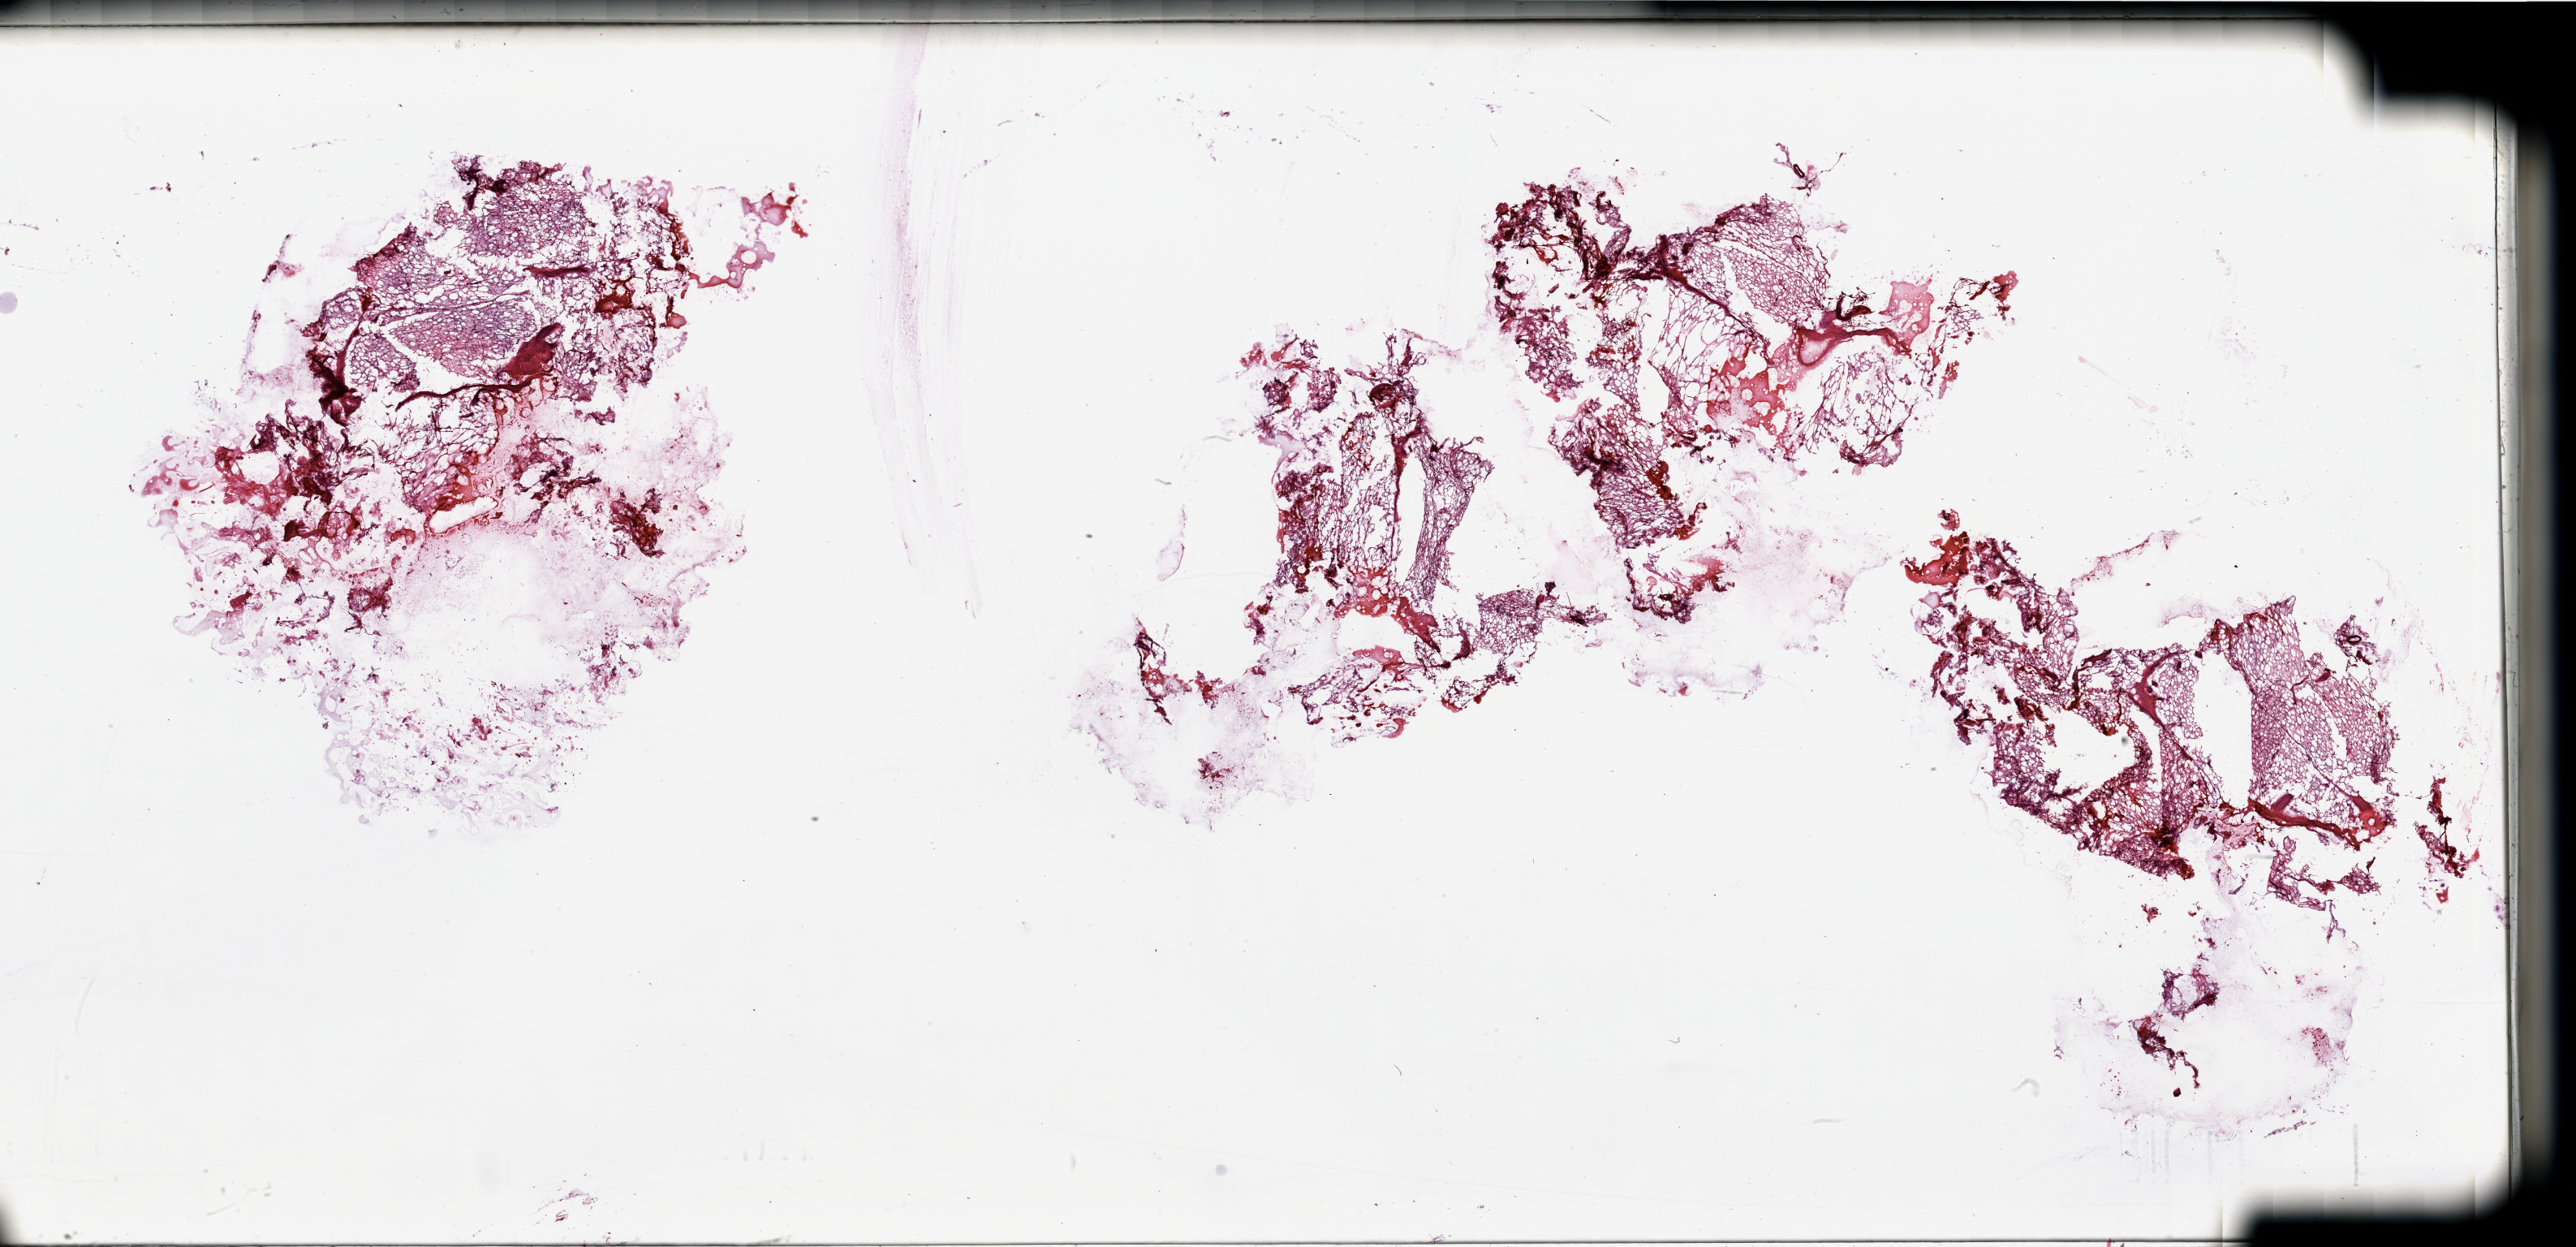
Whole-slide histology image, H&E — low-resolution overview of the scanned area, about 50.2 x 24.3 mm (slide scanned at 20x); tumour tissue sample, kidney. 74-year-old female patient. Histologic grade: G2 (moderately differentiated).
* histologic diagnosis: Renal cell carcinoma, NOS
* primary tumour site (as recorded): lower pole
* AJCC pathologic stage: I